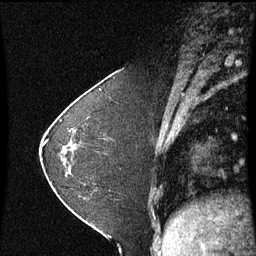
Breast MRI (dynamic contrast-enhanced), one sagittal slice. Slice 21 of 60 in the series (ordered by position). Dynamic contrast-enhanced series, image 2 of 3 at this slice position (ordered by acquisition). 1.5 T. TE 4.2 ms, TR 8.9 ms. 2 mm slice thickness. 256 × 256 image matrix. Female patient, age 37 years. Case-level facts recorded for this patient, not image findings: setting: breast cancer imaged before/during neoadjuvant chemotherapy; receptor status: HR-positive, HER2-negative.
Outlined on this slice (semi-automatically segmented with operator editing):
- analysis volume of interest (the breast-tissue region the enhancement analysis was run in; not a lesion): bounding box (x1, y1, x2, y2) in pixels: (60, 102, 122, 181)
- tumour enhancement mask (voxels above the 70 % enhancement threshold inside the analysis volume of interest): (61, 120, 72, 133)